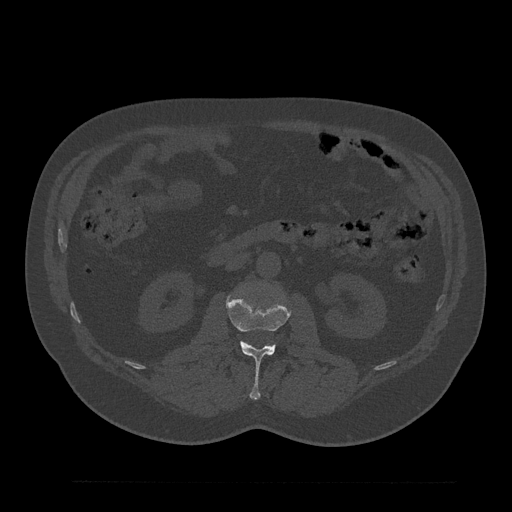
CT including the spine, one axial slice. Slice 89 of 797 in the series (ordered by position). Reconstruction kernel Br40s/3. Bone window (W 1800 / L 400 HU). 512 × 512 image matrix. Patient: male, 61 years. From the clinical record (not read from this slice): primary cancer: prostate.
Annotated regions visible in this slice (semi-automatic segmentation, software-assisted and operator-edited):
- L2 vertebra: box from (x=226, y=294) to (x=291, y=400) px